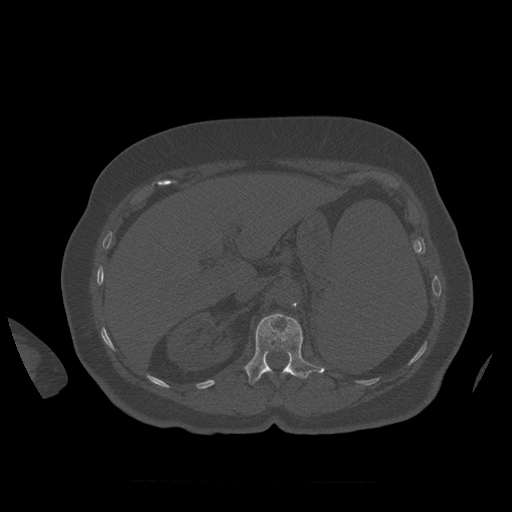
CT including the spine, one axial slice; position 282 of 399 along the scan axis; reconstruction kernel STANDARD; bone window (W 1800 / L 400 HU); 1.25 mm slice thickness; 512 × 512 image matrix, field of view 404 × 404 mm. Patient age 81 years. Case-level facts recorded for this patient, not image findings: primary cancer: renal; vertebrae with lytic lesions (as recorded): L1.
Structures marked on this image (semi-automatic segmentation, software-assisted and operator-edited):
- L1 vertebra: bounding box (x1, y1, x2, y2) in pixels: (244, 314, 325, 384)